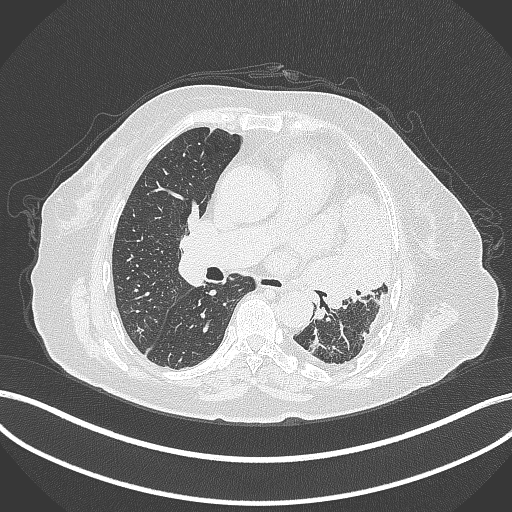
Chest CT, one axial slice; lung window (W 1500 / L -600 HU); 1 mm slice thickness; 512 × 512 image matrix, field of view 400 × 400 mm. Patient: female, 75 years. Case-level facts recorded for this patient, not image findings: clinical TNM (as recorded): T3 N3 M1.
Structures marked on this image (bounding box drawn by a radiologist):
- lung tumour (recorded histology: adenocarcinoma): bounding box (x1, y1, x2, y2) in pixels: (308, 190, 394, 312)